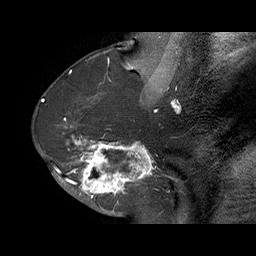
Breast MRI (dynamic contrast-enhanced), one sagittal slice; slice 33 of 70 in the series (ordered by position); dynamic contrast-enhanced series, time point 2 of 6 at this slice position (early post-contrast); 1.5 T; TE 4.5 ms, TR 32.4 ms; 3 mm slice thickness; 256 × 256 image matrix, field of view 180 × 180 mm. Female patient. From the clinical record (not read from this slice): setting: breast cancer imaged before/during neoadjuvant chemotherapy; receptor status: HR-positive, HER2-negative.
Annotated regions visible in this slice (semi-automatically segmented with operator editing):
- analysis volume of interest (the breast-tissue region the enhancement analysis was run in; not a lesion): bounding box (x1, y1, x2, y2) in pixels: (71, 128, 159, 202)
- tumour enhancement mask (voxels above the 100 % enhancement threshold inside the analysis volume of interest): (71, 135, 153, 202)